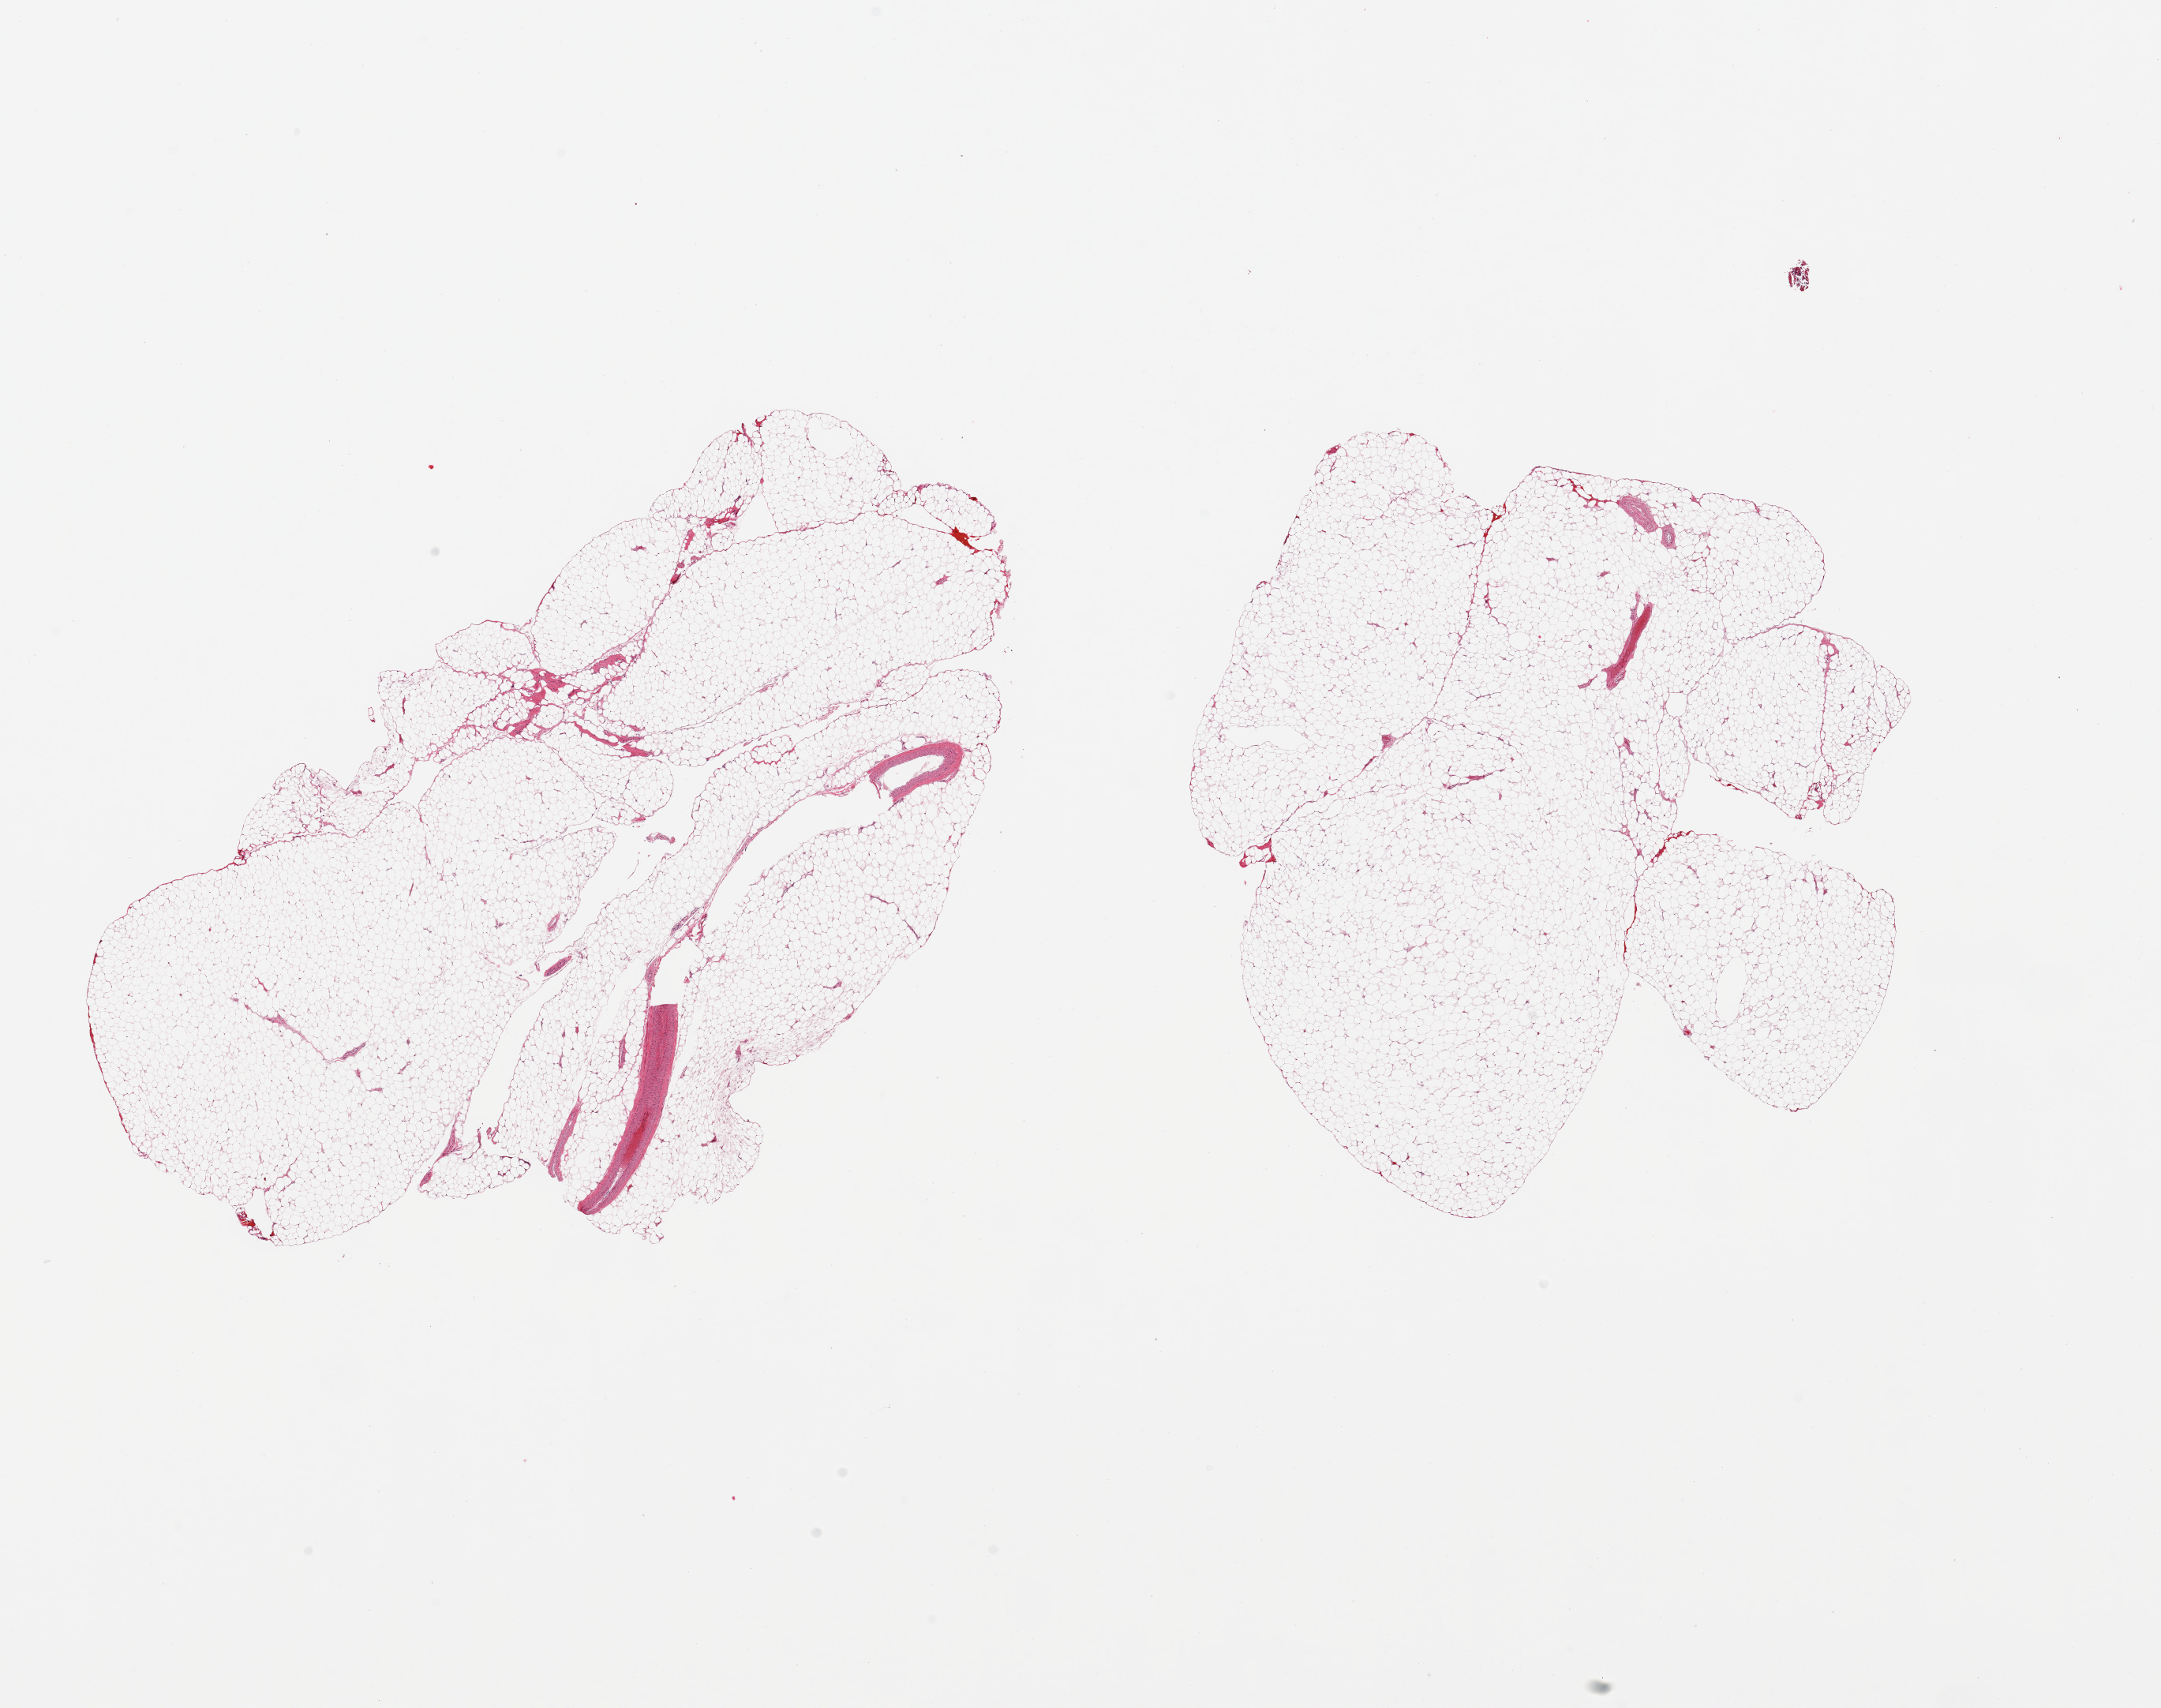
Digitized hematoxylin and eosin (H&E)-stained section, brightfield, whole scanned area (about 21.7 x 17.1 mm) shown as a low-resolution overview, PAXgene-fixed paraffin-embedded (PFPE) section, section of omentum (target tissue), donor tissue sample. Donor sex: male.
Pathologist's review note for this sample: 2 pieces, trace vascular elements.